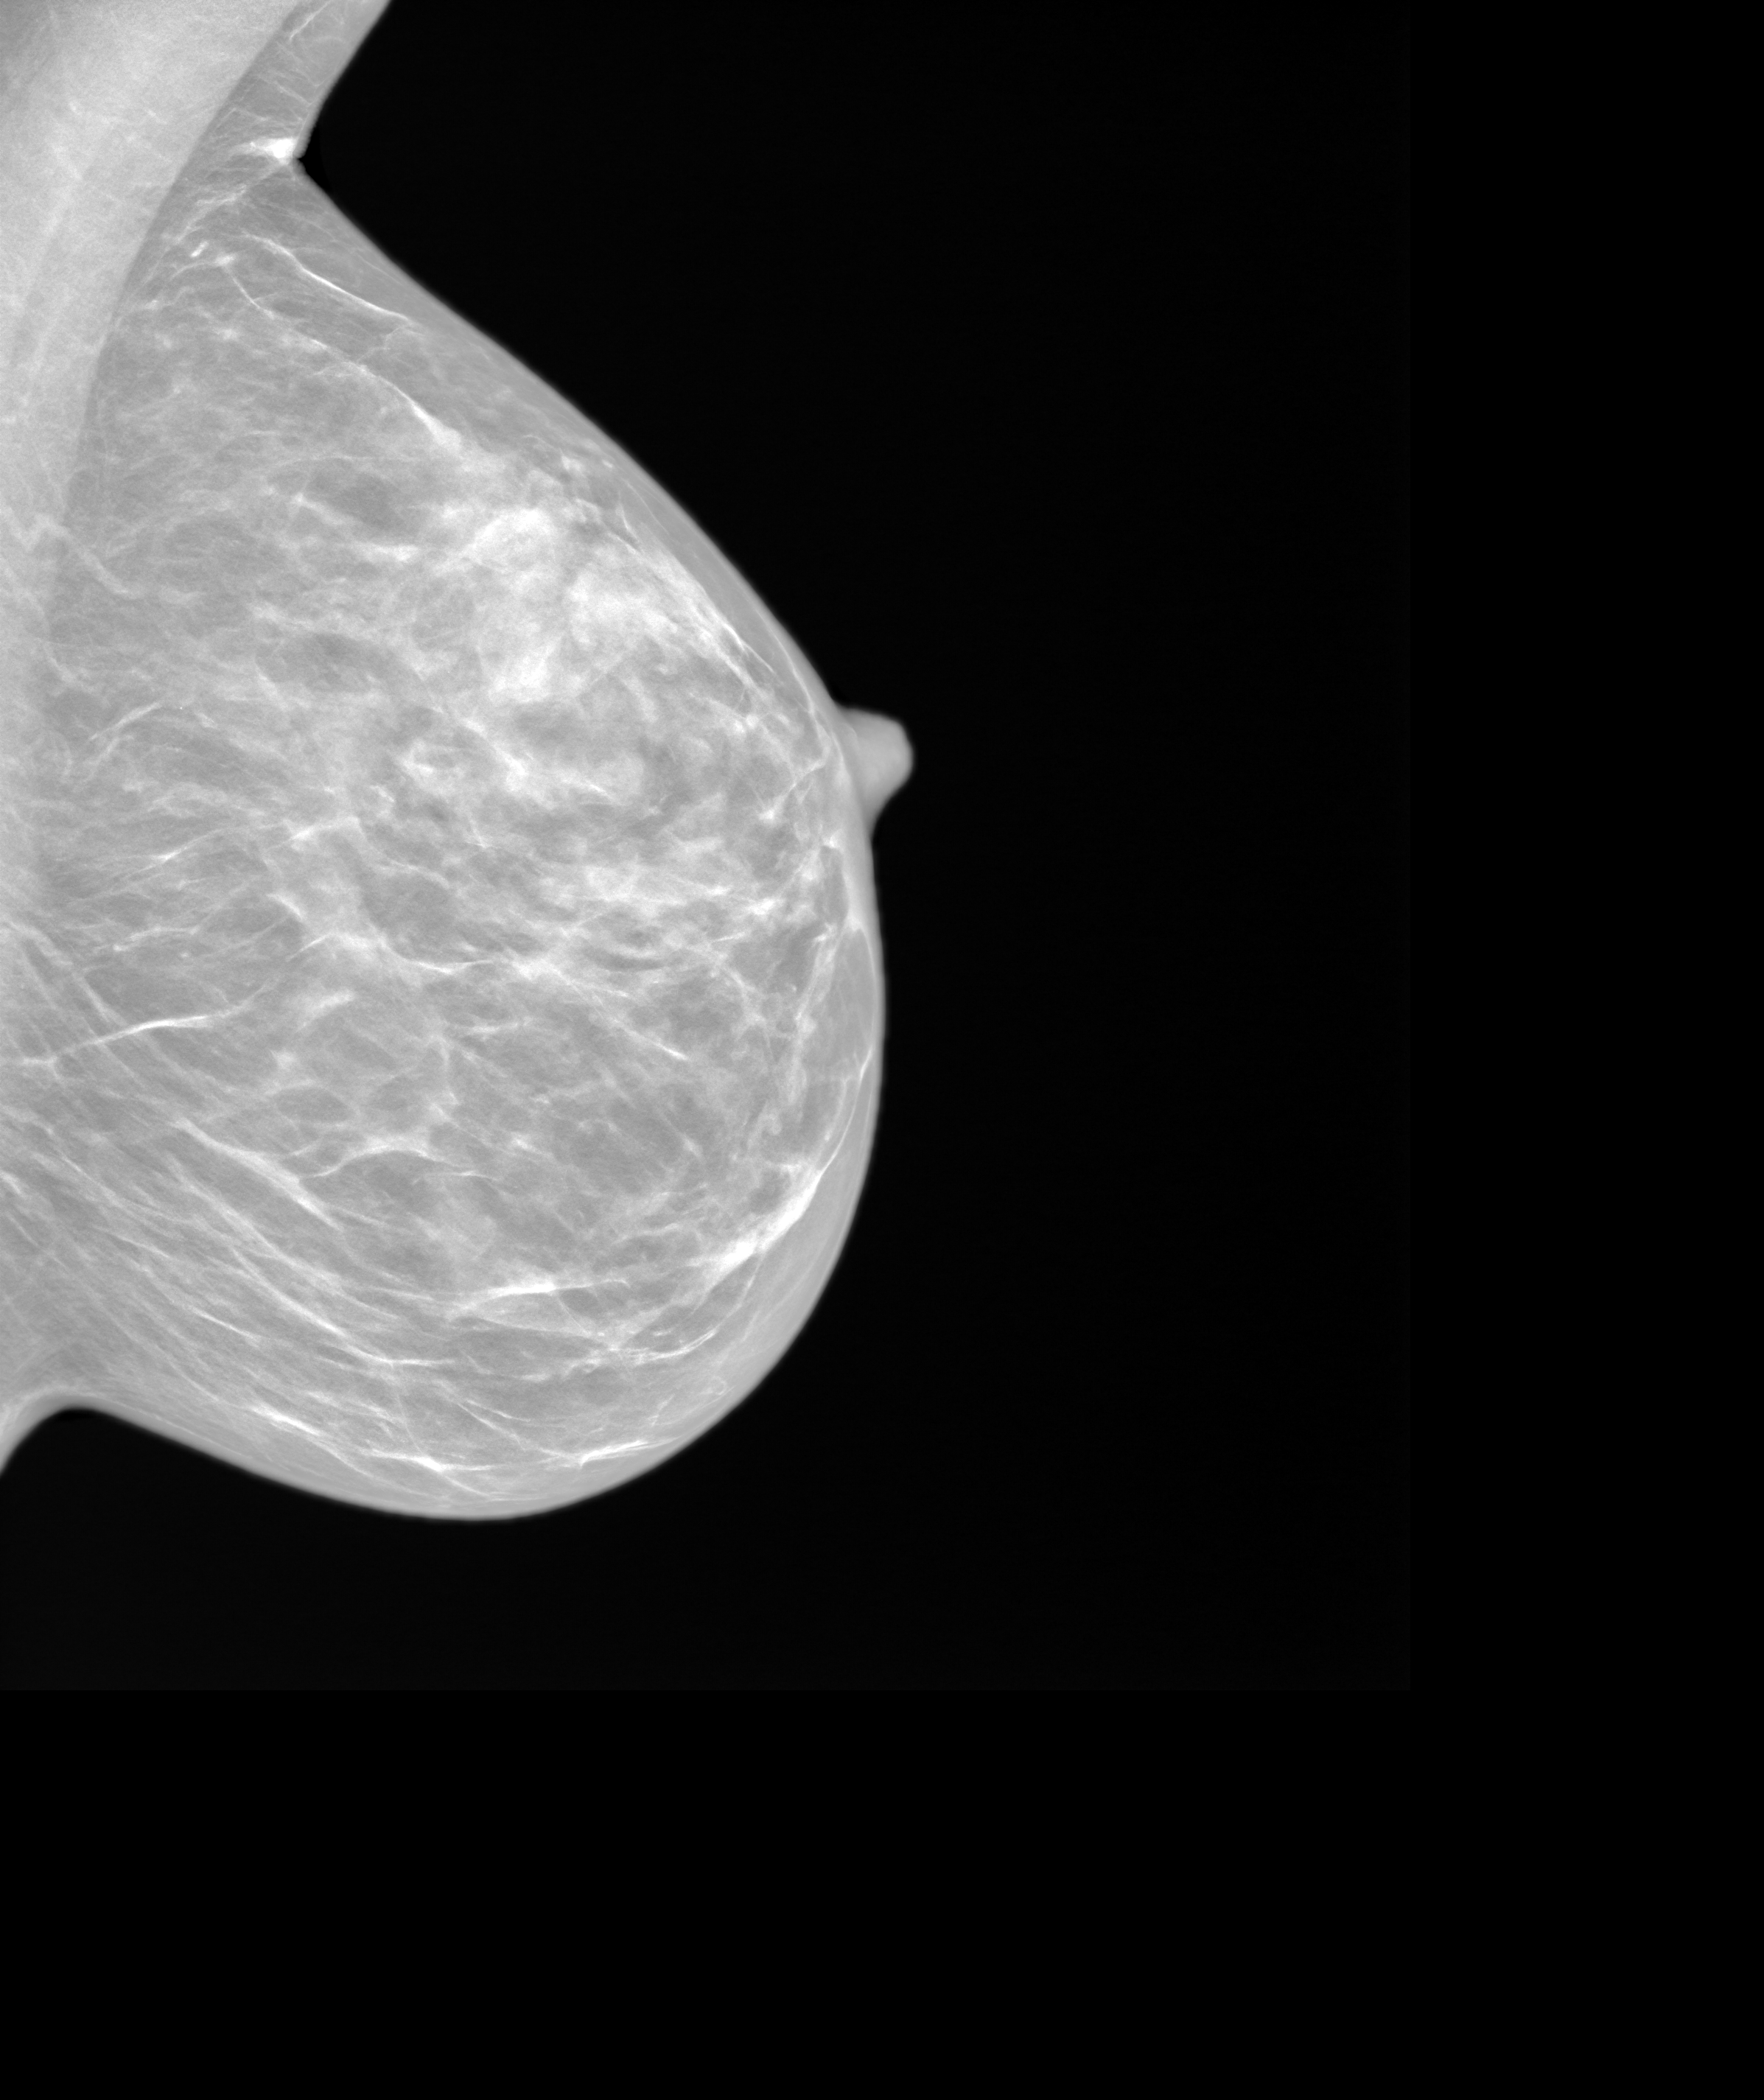
Screening examination, system: SenoIris_1SP1.1(421). Female patient, age 57 years.
Image type: synthesized 2-D view from tomosynthesis. Breast: left. Projection: mediolateral oblique (MLO) view.